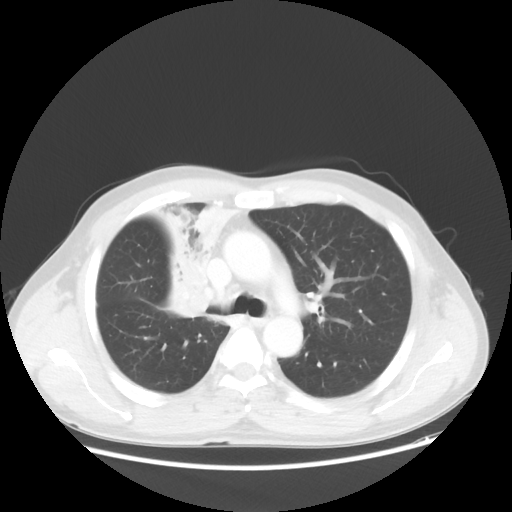
Chest CT, one axial slice; position 36 of 56 along the scan axis; lung window (W 1500 / L -600 HU); 512 × 512 image matrix, field of view 398 × 398 mm. Patient: male, 60 years. From the clinical record (not read from this slice): clinical TNM (as recorded): T2a N1 M0.
Annotated regions visible in this slice (rectangle marked by the reading radiologist):
- lung tumour (recorded histology: squamous cell carcinoma): bounding box <136,186,242,321> (left, top, right, bottom; pixels)